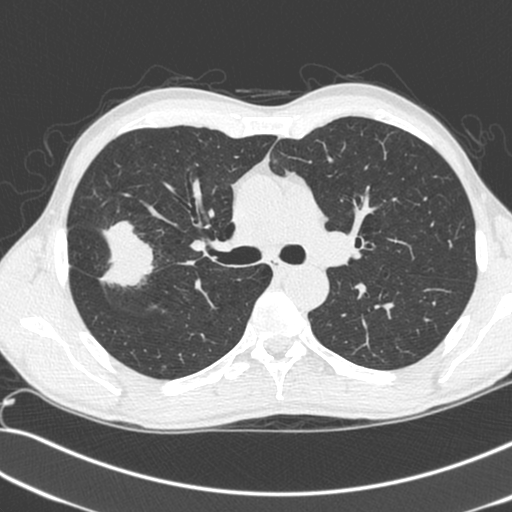
Low-dose screening chest CT, axial slice. First (baseline) screen. Lung window (W 1500 / L -600 HU). 120 kVp. Slice 91 of 281 in the series. Male, age 55 years at enrolment. Current smoker at enrolment.
Lesion marked by an expert reader, bounding box [x1, y1, x2, y2] px = [67, 220, 156, 297]. Screening reader's record for this exam (one nodule recorded; not confirmed to be the boxed lesion): non-calcified nodule or mass ≥4 mm, right upper lobe, 52 × 39 mm, spiculated (stellate) margins, soft tissue attenuation. Participant outcome: lung cancer diagnosed 25 days after this screen — large cell neuroendocrine carcinoma, right upper lobe, poorly differentiated (G3), stage IIB (AJCC 6th edition), 49 mm at pathology.